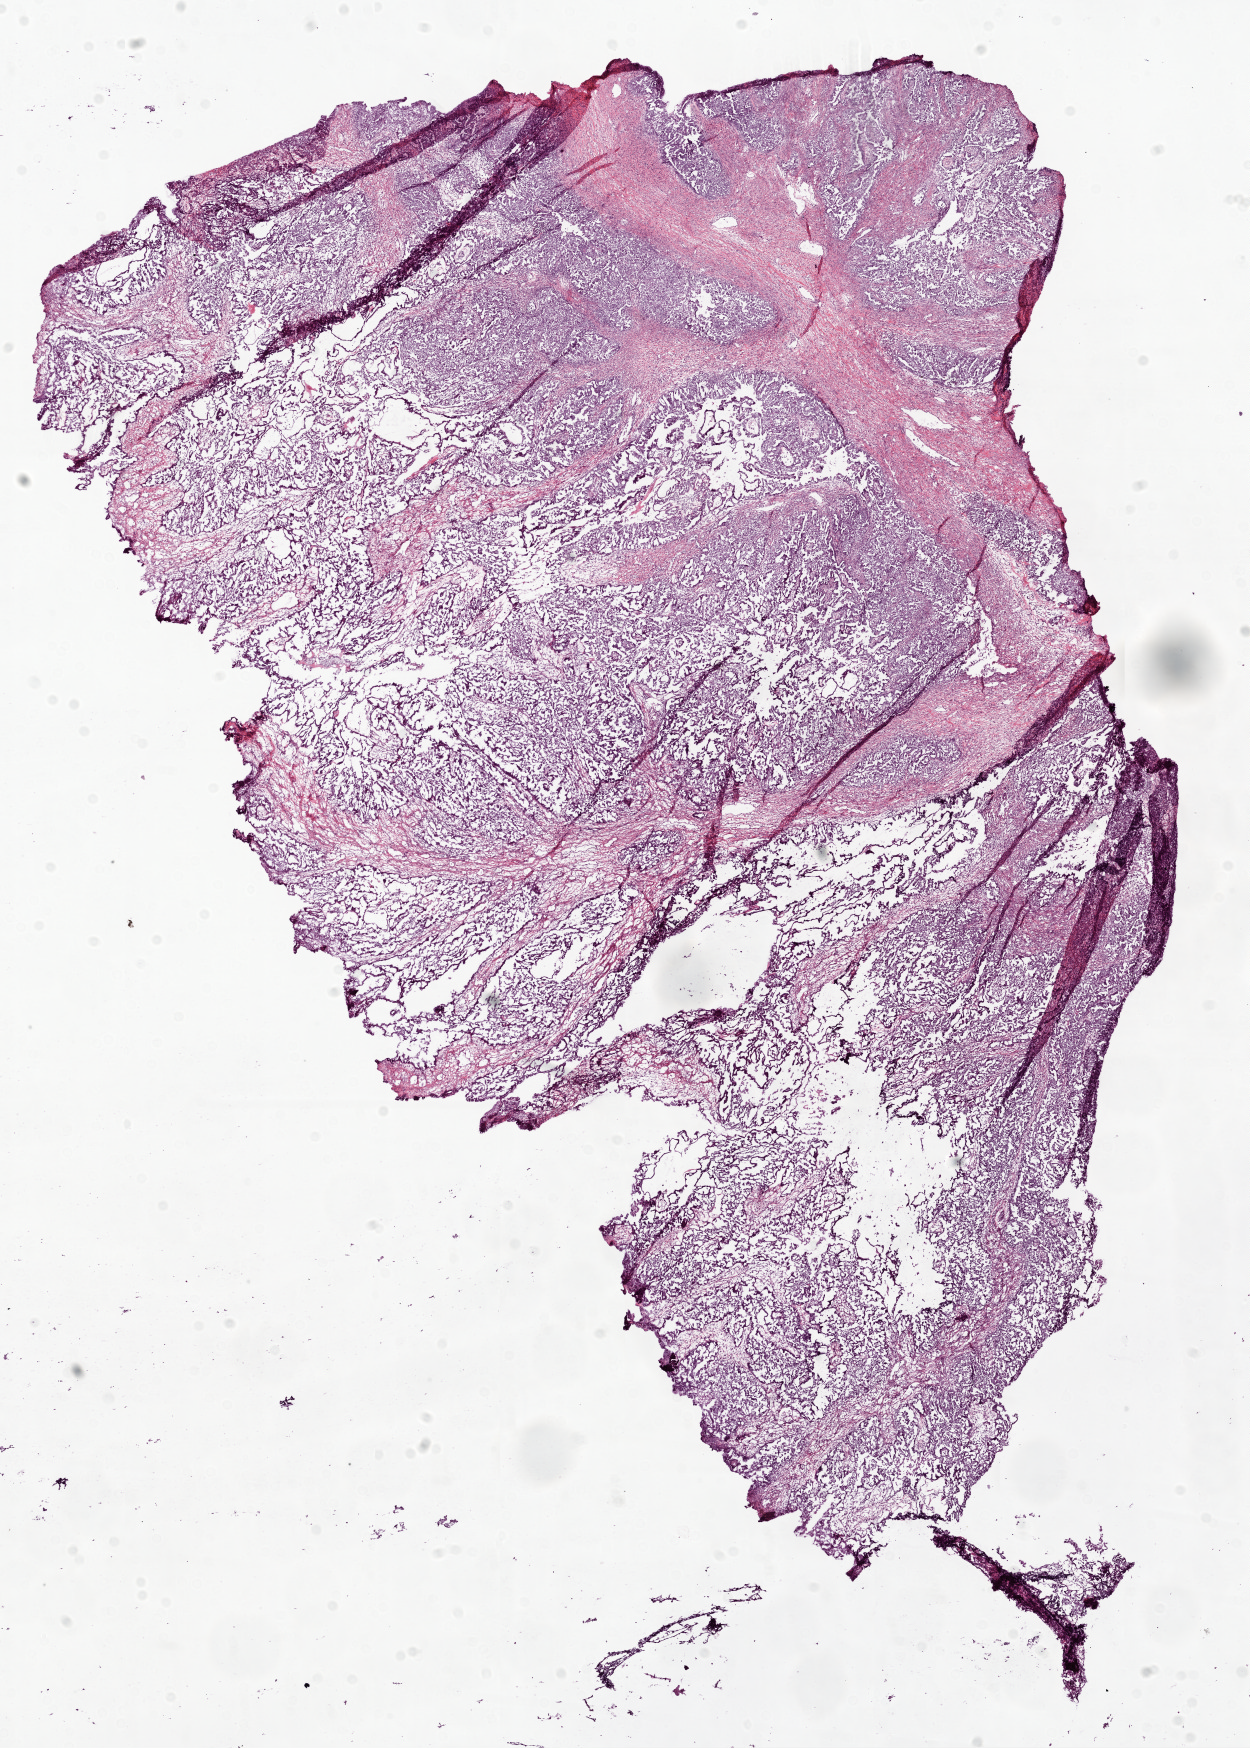
Whole-slide histology image, H&E-stained, whole scanned area (about 10.0 x 14.0 mm, acquisition: 20x scan) shown as a low-resolution overview, frozen section from the top of the tissue portion, primary tumour sample from the ovary. Female, age 78 years at initial diagnosis. Histologic grade: G3 (poorly differentiated). Pathologist review of this section (percent, as recorded): tumour cells 89%, tumour nuclei 90%, normal cells 0%, stromal cells 10%, necrosis 1%.
- FIGO stage: IIIC
- pathologic diagnosis: Serous cystadenocarcinoma, NOS